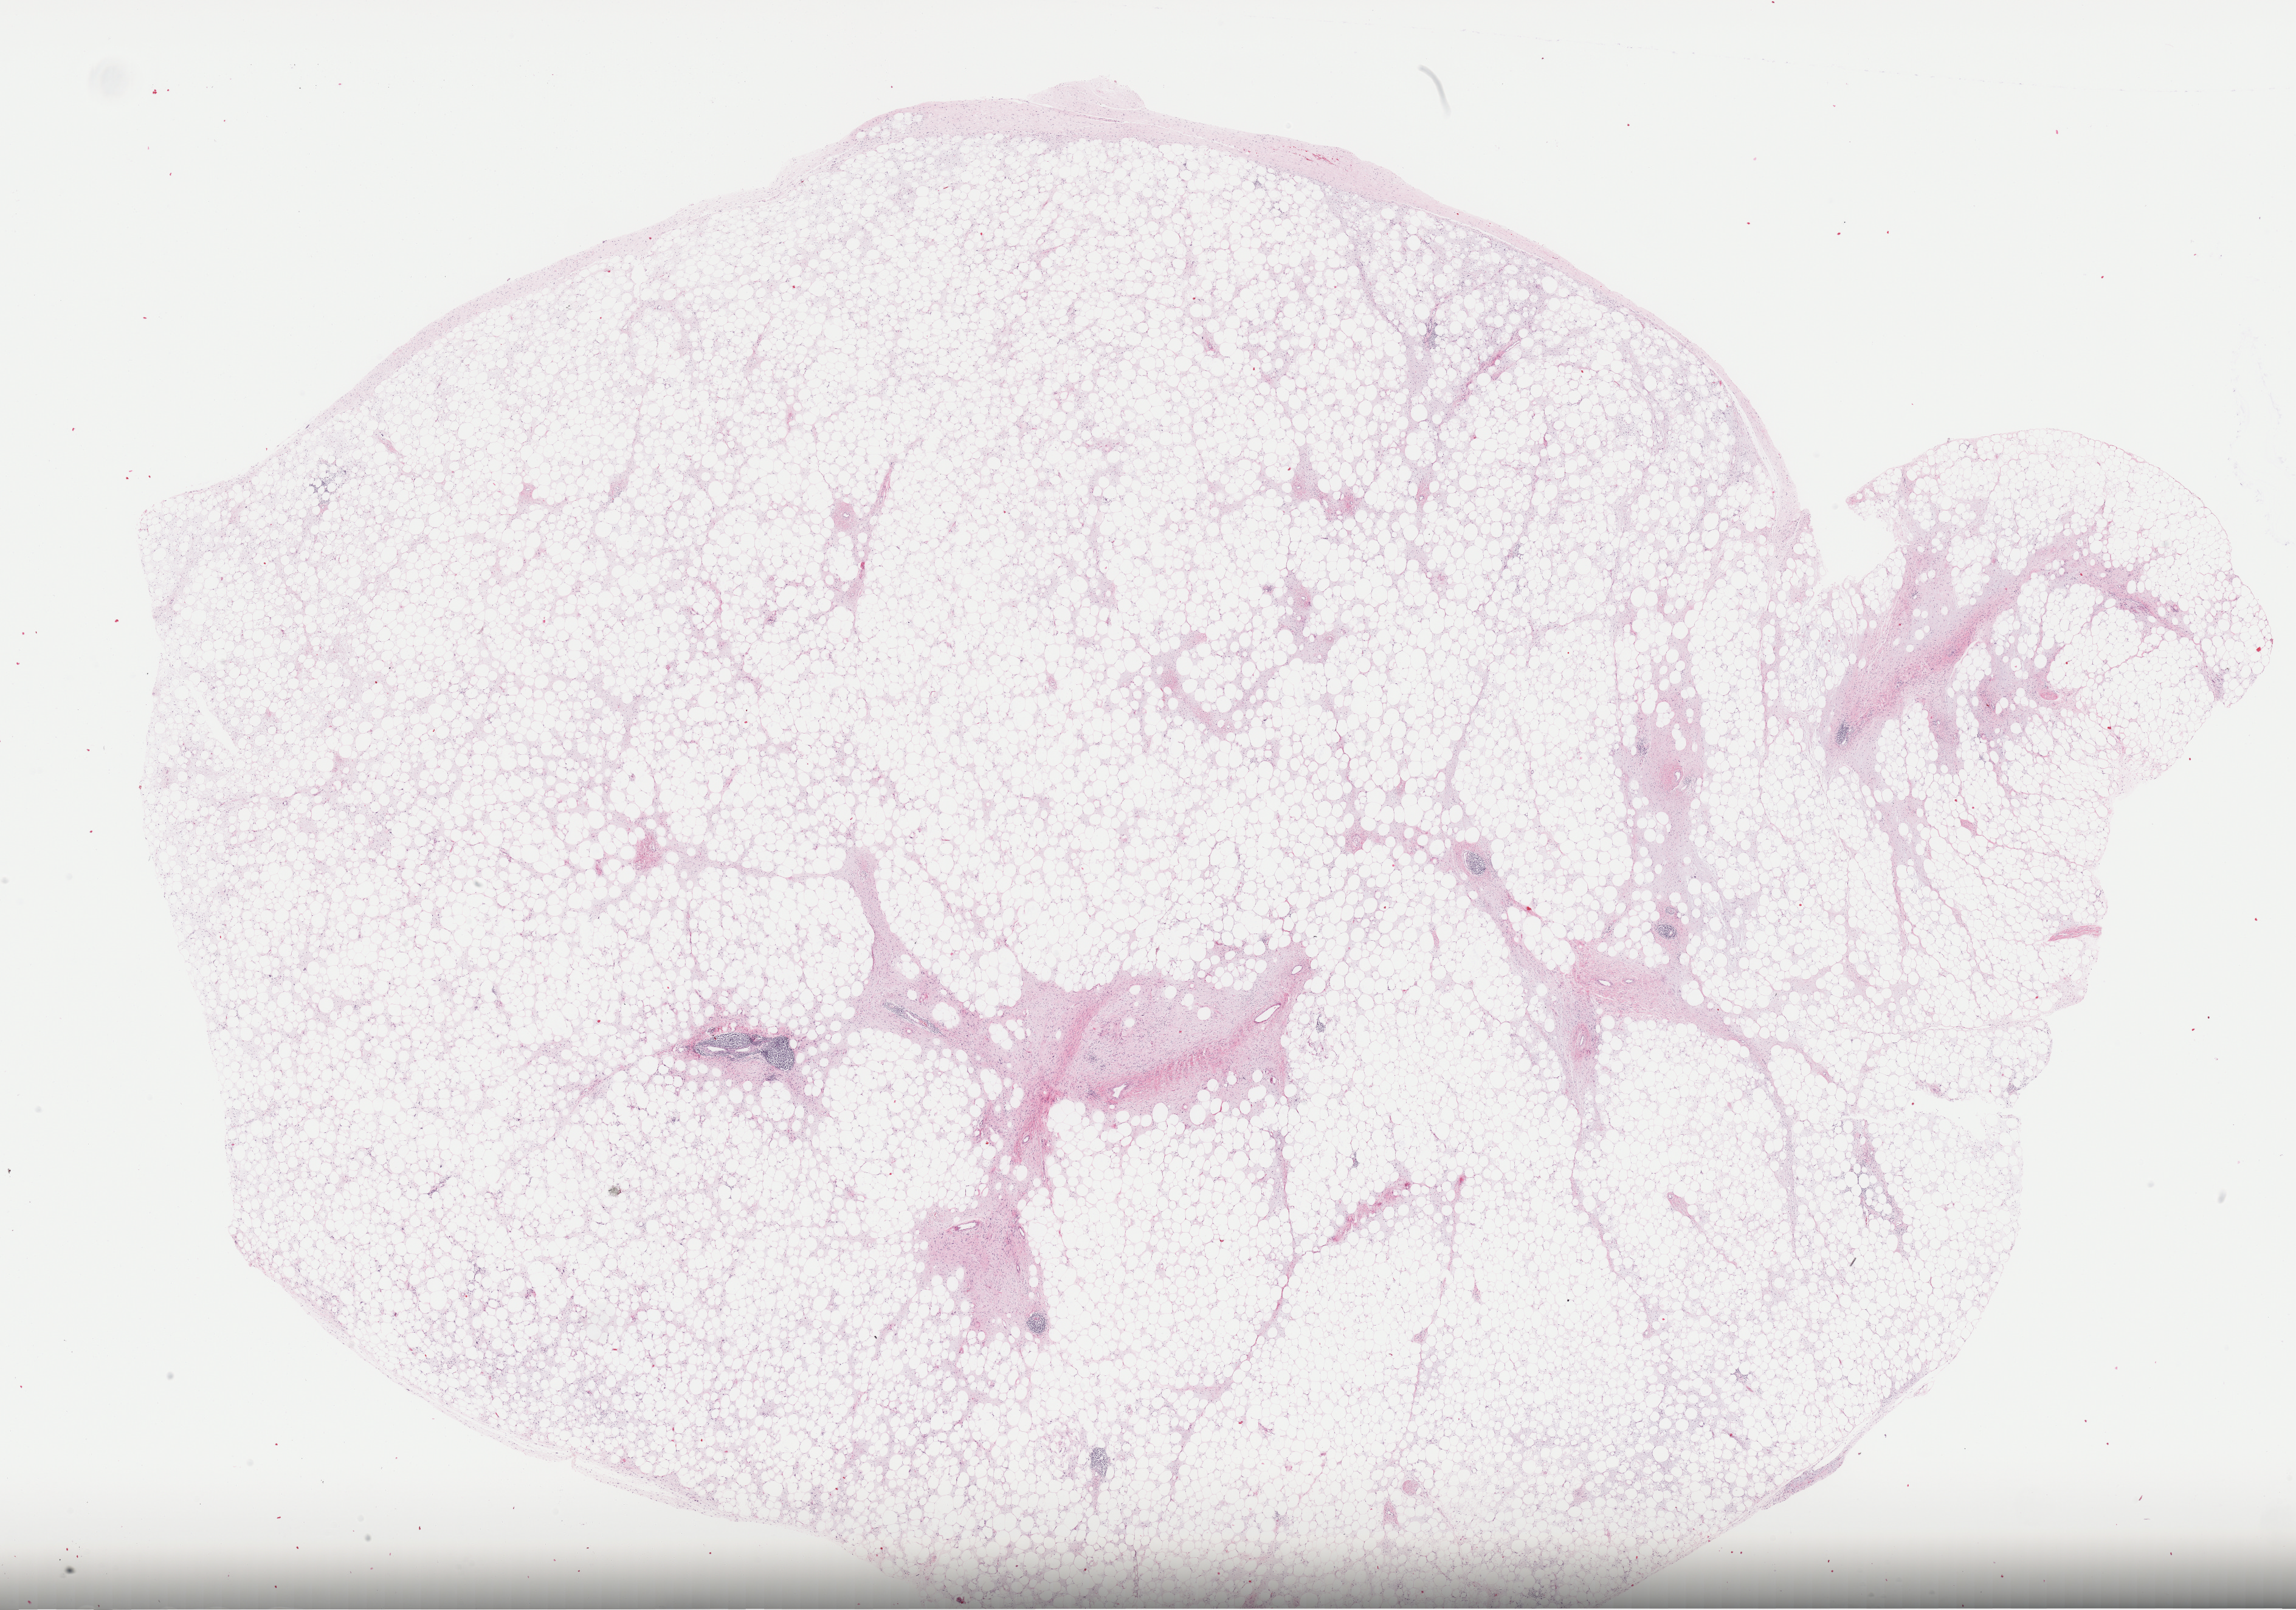
H&E whole-slide image — whole scanned area (about 30.2 x 21.2 mm) shown as a low-resolution overview, formalin-fixed paraffin-embedded (FFPE) diagnostic section, primary tumour sample from the retroperitoneum and peritoneum. Patient: male, age at initial diagnosis 77 years.
Histologic diagnosis: Dedifferentiated liposarcoma (retroperitoneum).